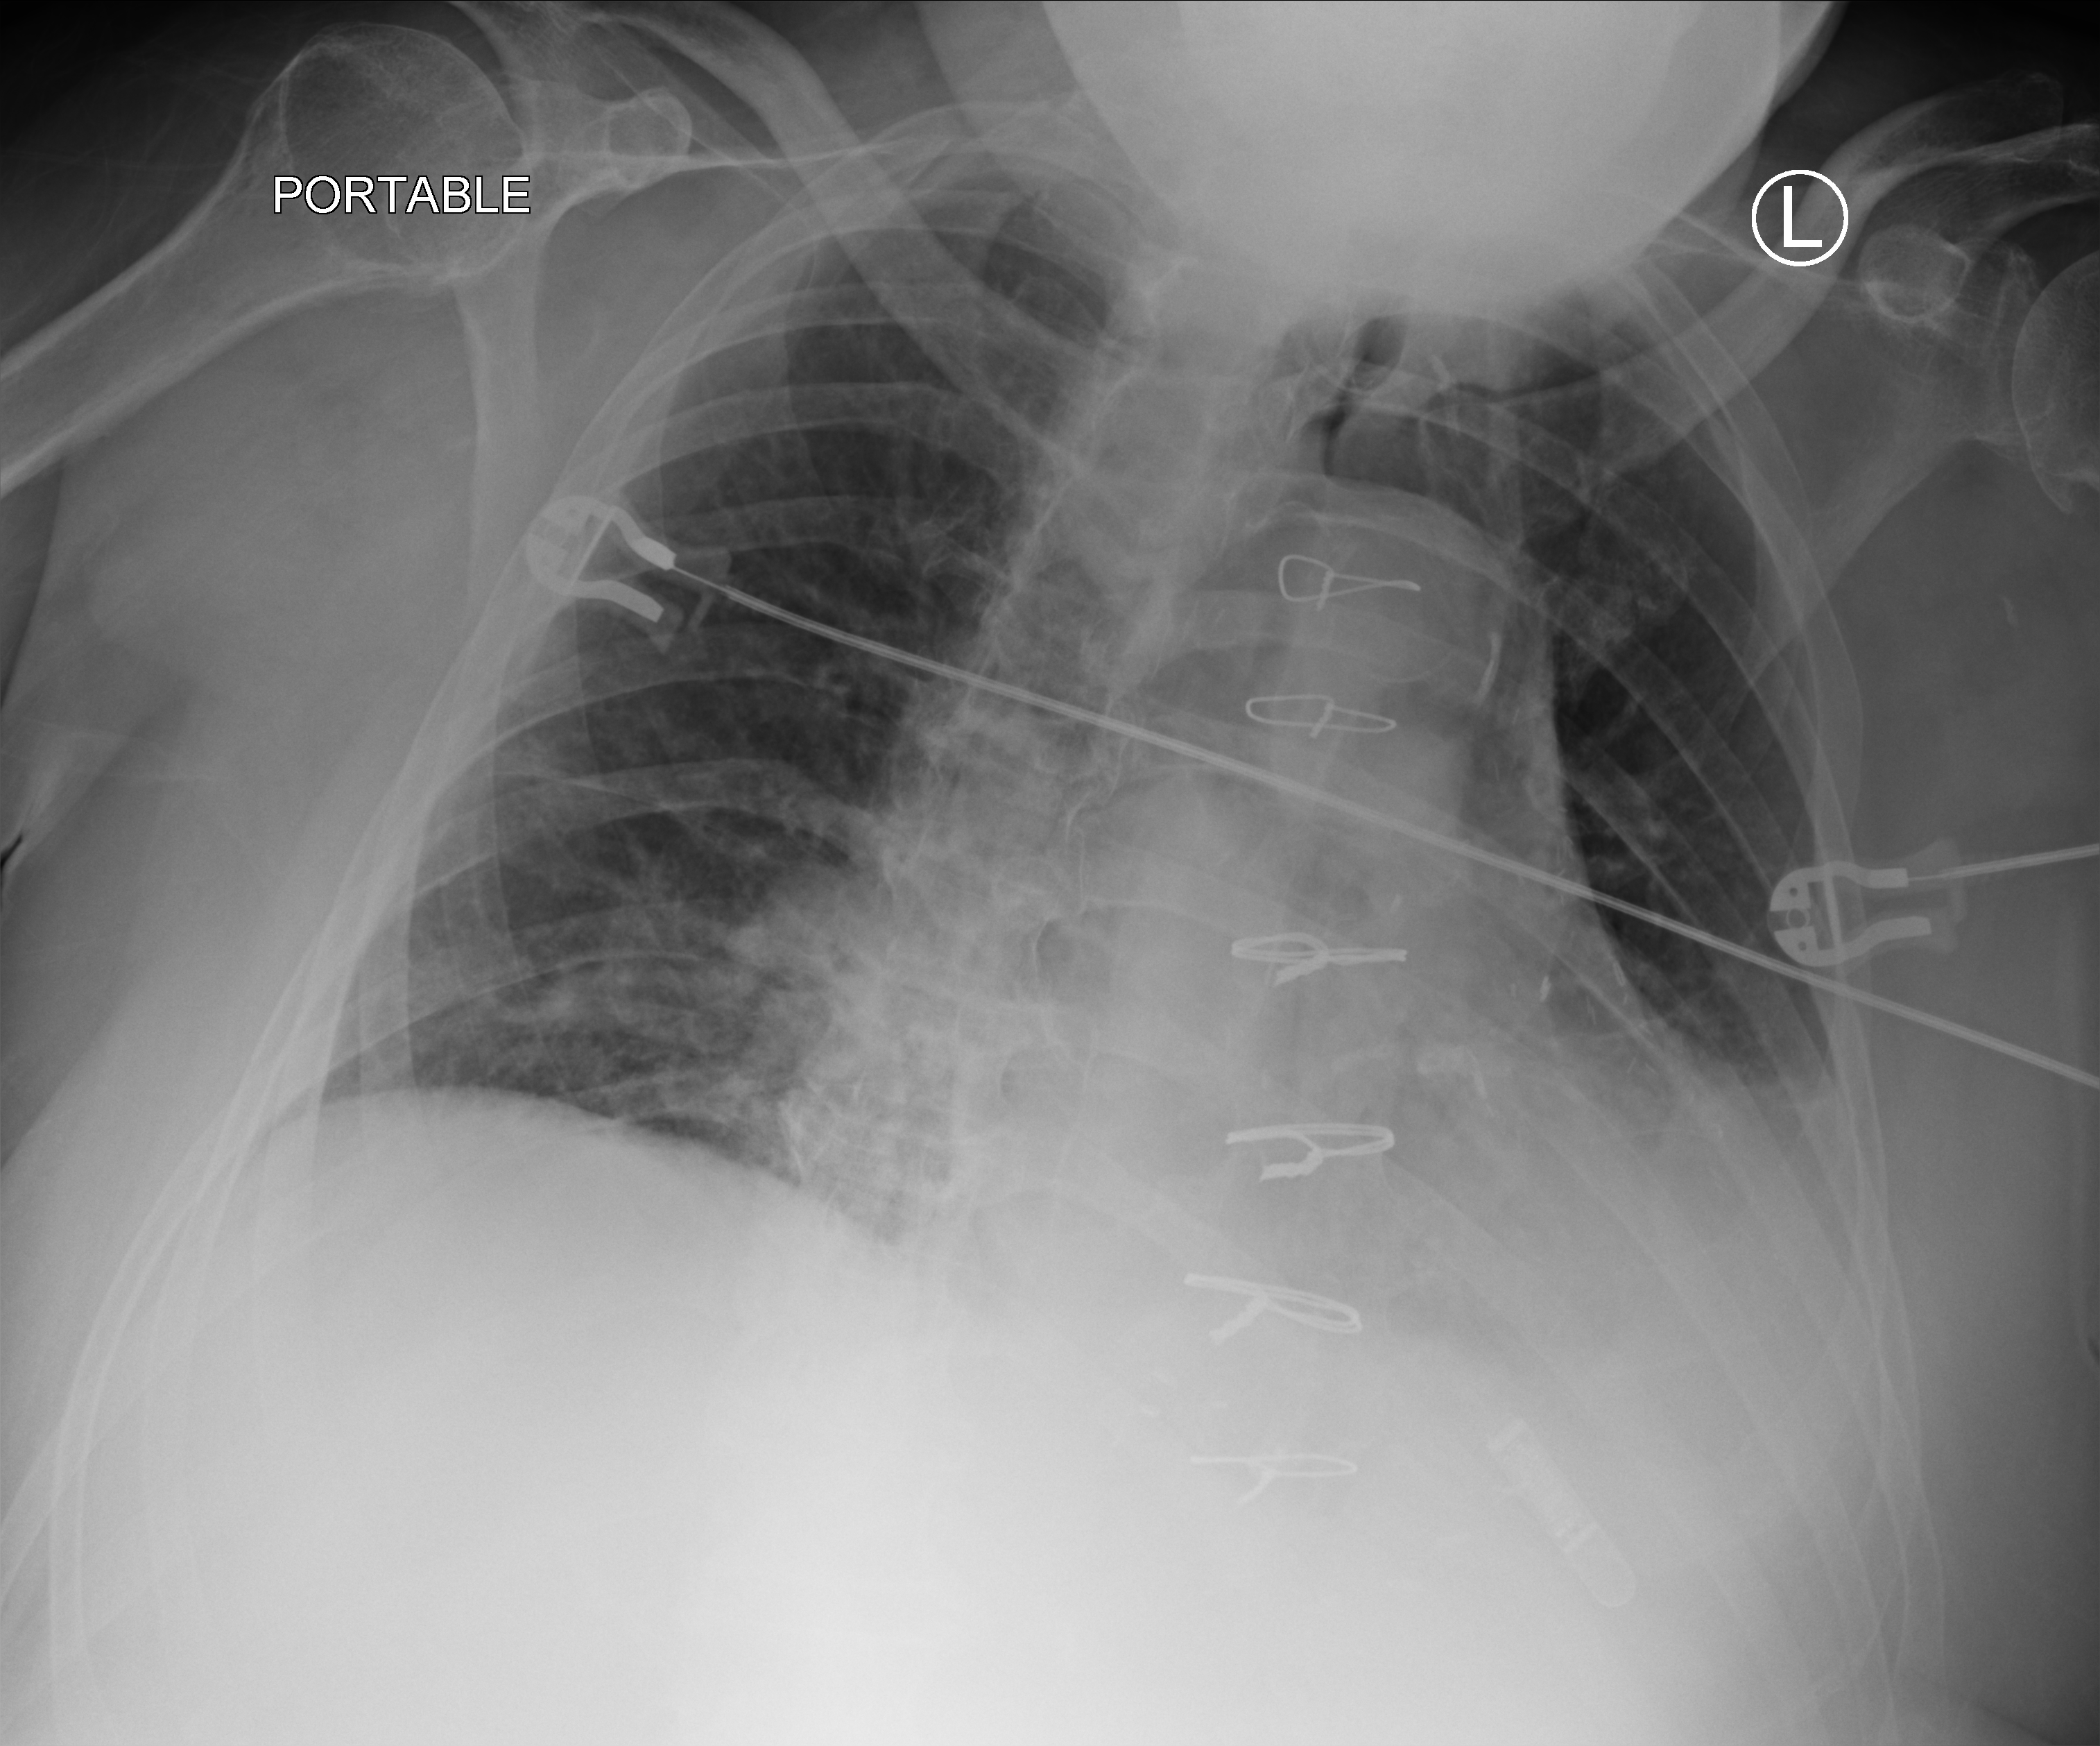
Bedside chest radiograph (computed radiography), anteroposterior (AP) projection. Male patient hospitalised with COVID-19, age 60–74 years.
Hospital-stay facts (about this admission, not read from this image; timing relative to this image not recorded): admitted to intensive care during this hospital stay: no; mechanically ventilated during this hospital stay: no.